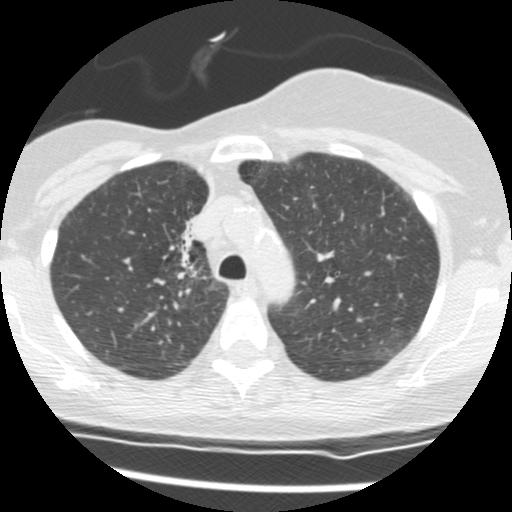
Low-dose screening chest CT, axial slice, second screening round (one year after baseline), lung window (W 1500 / L -600 HU), 2.5 mm slice thickness, standard (soft-tissue) reconstruction kernel (STANDARD), 120 kVp, slice 34 of 165 in the series. Female participant, aged 56 years at enrolment. Current smoker at enrolment.
Expert reader's lesion annotation, bounding box [x1, y1, x2, y2] px = [155, 208, 215, 281]. The screening reader recorded 2 non-calcified nodules or masses ≥4 mm on this exam (right middle lobe, right lower lobe); which of them this box marks is not recorded. Official screen result: positive, change unspecified: nodule(s) >= 4 mm or enlarging nodule(s), mass(es), or other non-specific abnormalities suspicious for lung cancer. Later outcome: lung cancer diagnosed 675 days after this screen — adenocarcinoma, NOS, right upper lobe, stage IIIB (AJCC 6th edition), 8 mm at pathology.